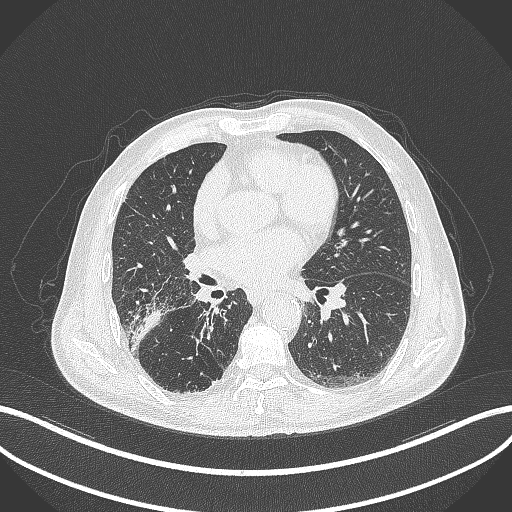
Chest CT, one axial slice; reconstruction kernel B70f; 120 kVp; lung window (W 1500 / L -600 HU); 1 mm slice thickness; 512 × 512 image matrix, field of view 400 × 400 mm. Patient: male, 72 years. From the clinical record (not read from this slice): clinical TNM (as recorded): T3 N2 M0.
Outlined on this slice (rectangle marked by the reading radiologist):
- lung tumour (recorded histology: adenocarcinoma): bounding box (x1, y1, x2, y2) in pixels: (132, 307, 165, 333)